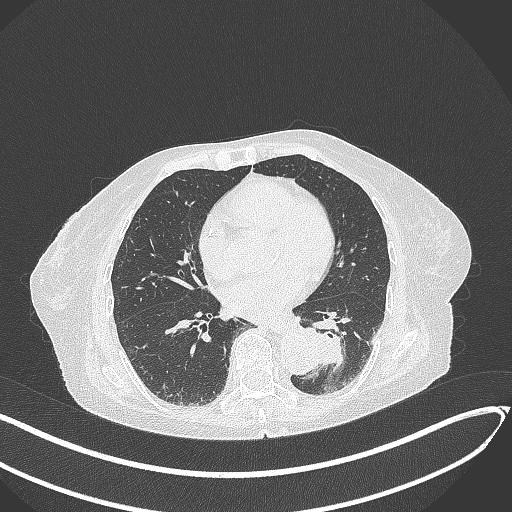
Chest CT, one axial slice; position 104 of 324 along the scan axis; lung window (W 1500 / L -600 HU); 512 × 512 image matrix, field of view 400 × 400 mm. Female patient, age 82 years. From the clinical record (not read from this slice): clinical TNM (as recorded): T1b N0 M1.
Structures marked on this image (rectangle marked by the reading radiologist):
- lung tumour (recorded histology: adenocarcinoma): bounding box (x1, y1, x2, y2) in pixels: (296, 321, 351, 371)